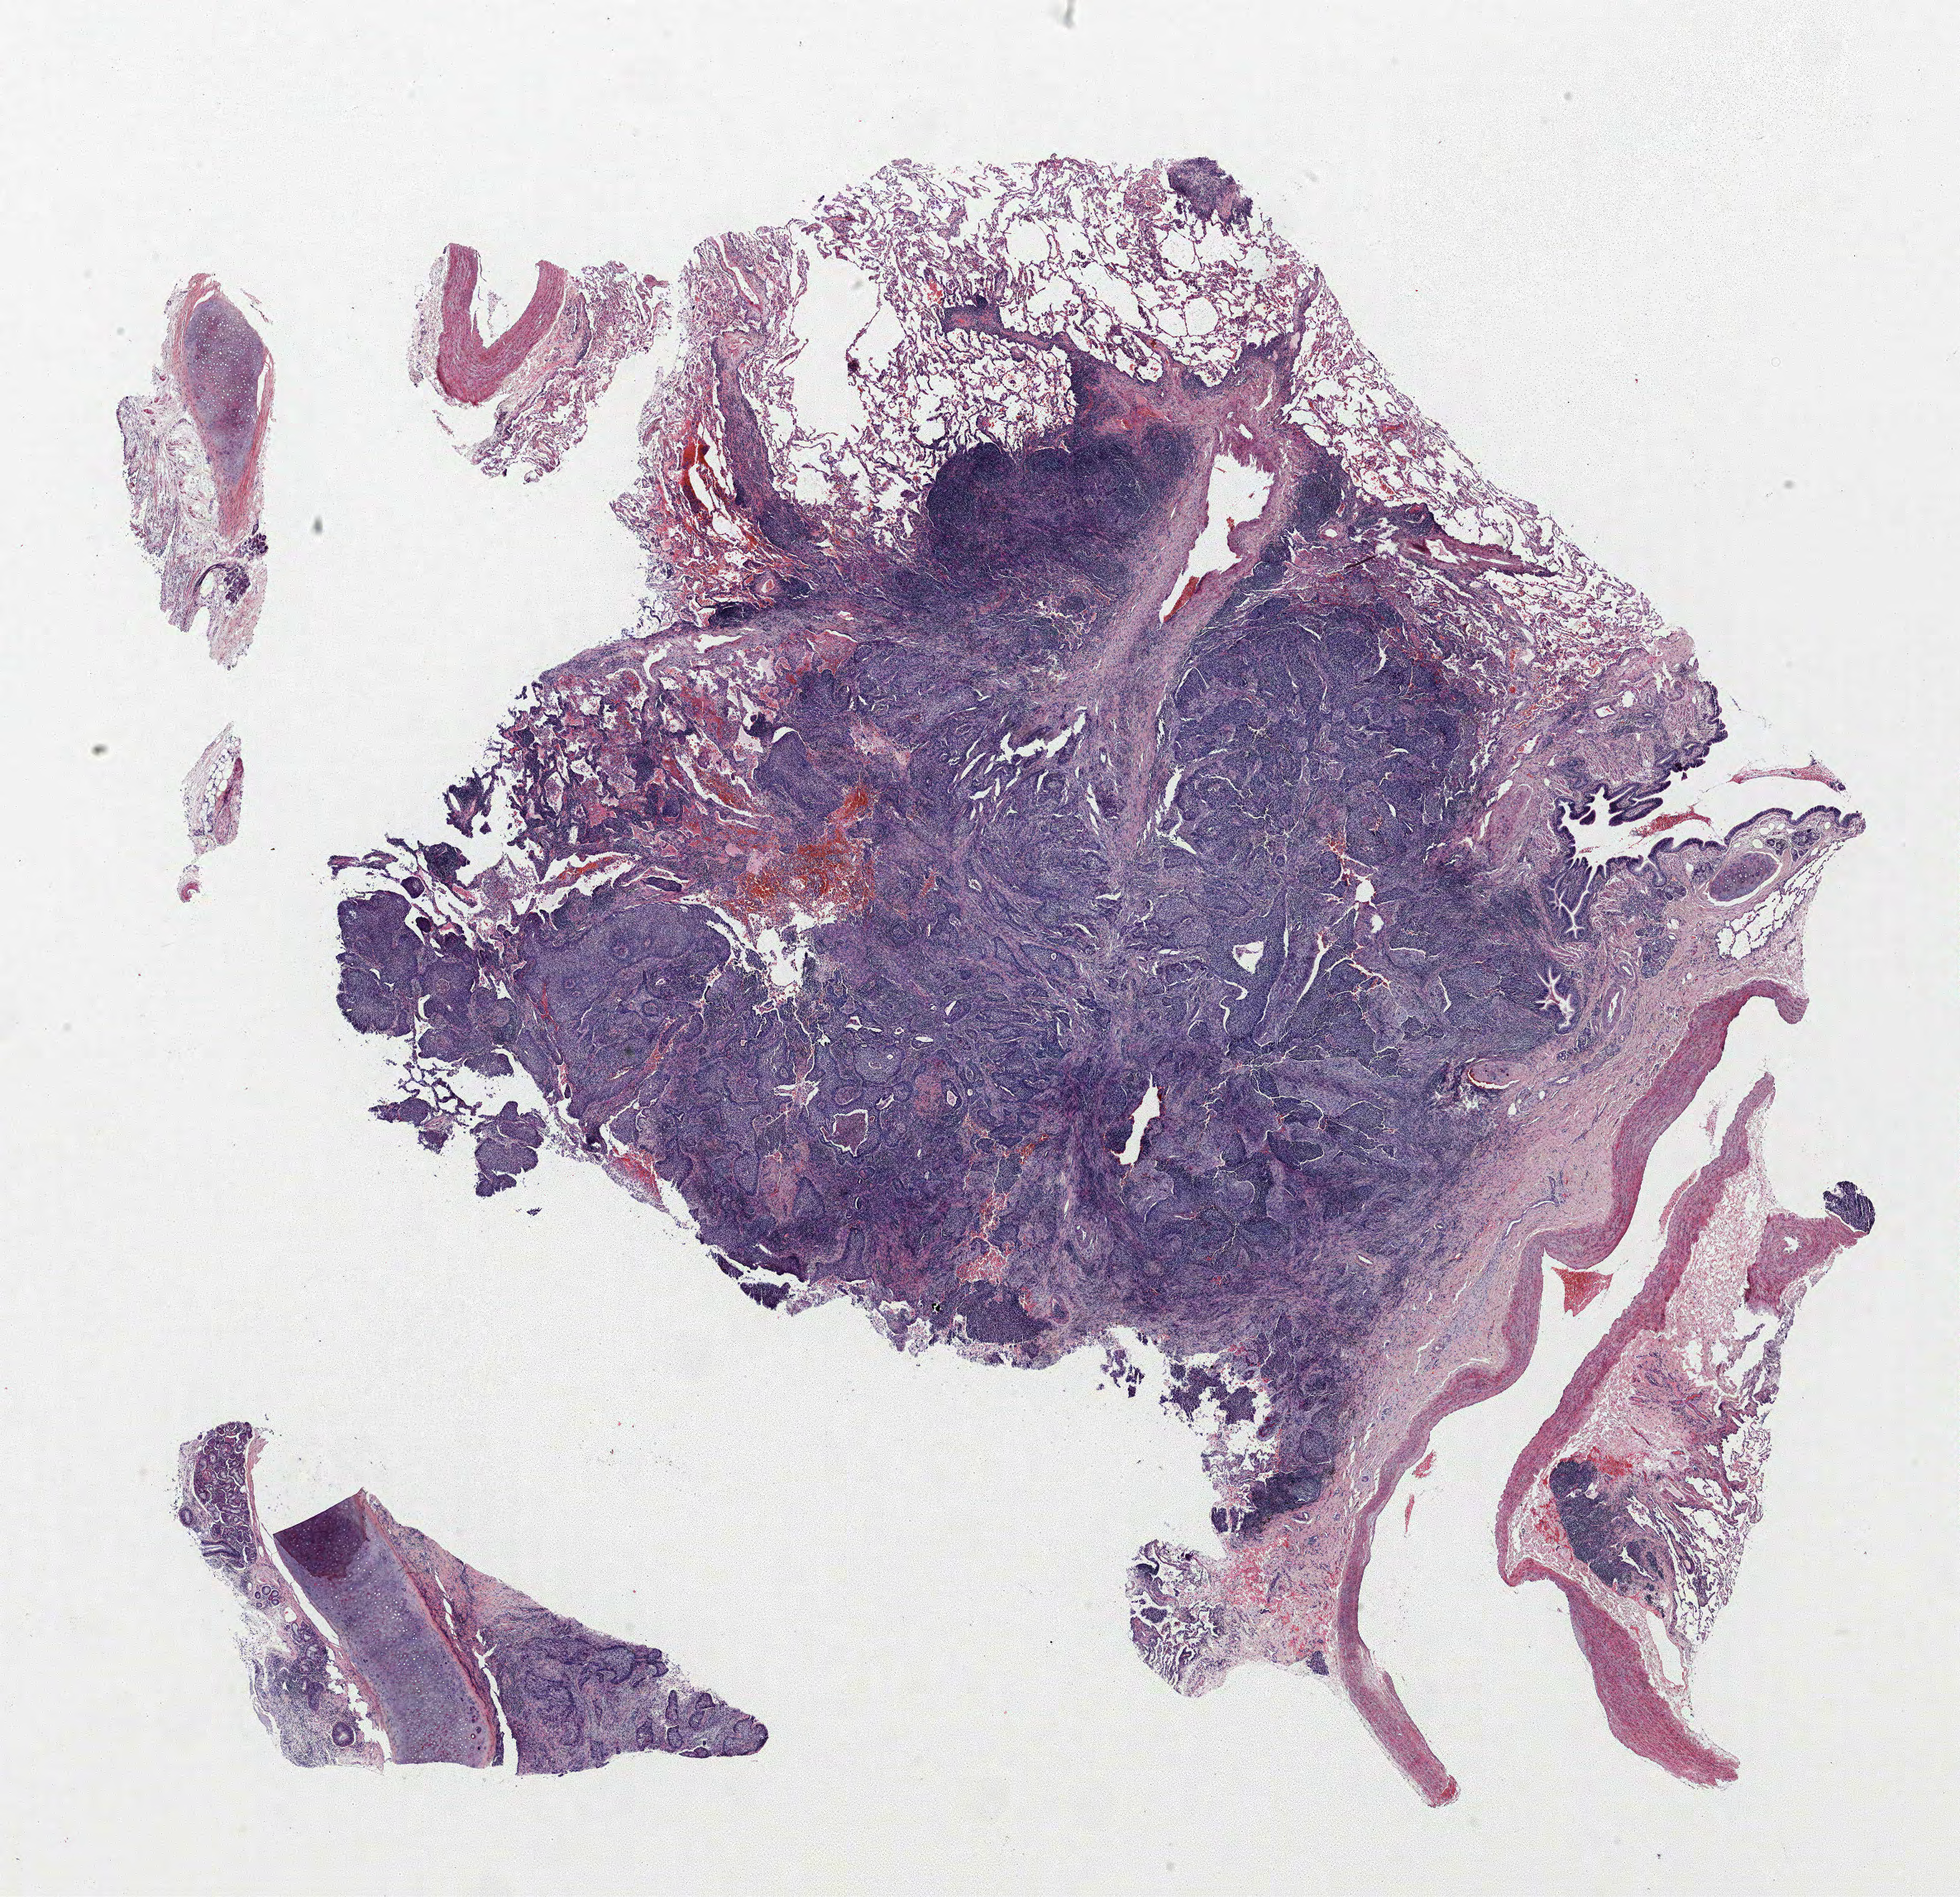
Whole-slide histology image, Hematoxylin and eosin (H&E) stained, shown as a low-resolution overview of the whole scanned area (about 19.0 x 18.4 mm), FFPE section, lung. Male, age 63 at enrolment. Former smoker at enrolment. Grade: moderately differentiated (G2).
* tumour size (pathology): 23 mm
* stage (AJCC 6th edition): IA
* participant's lung-cancer diagnosis: Squamous cell carcinoma, NOS (ICD-O-3 8070/3)
* ICD-O-3 topography: upper lobe of lung (C34.1)
* primary tumour location (clinical record): left upper lobe